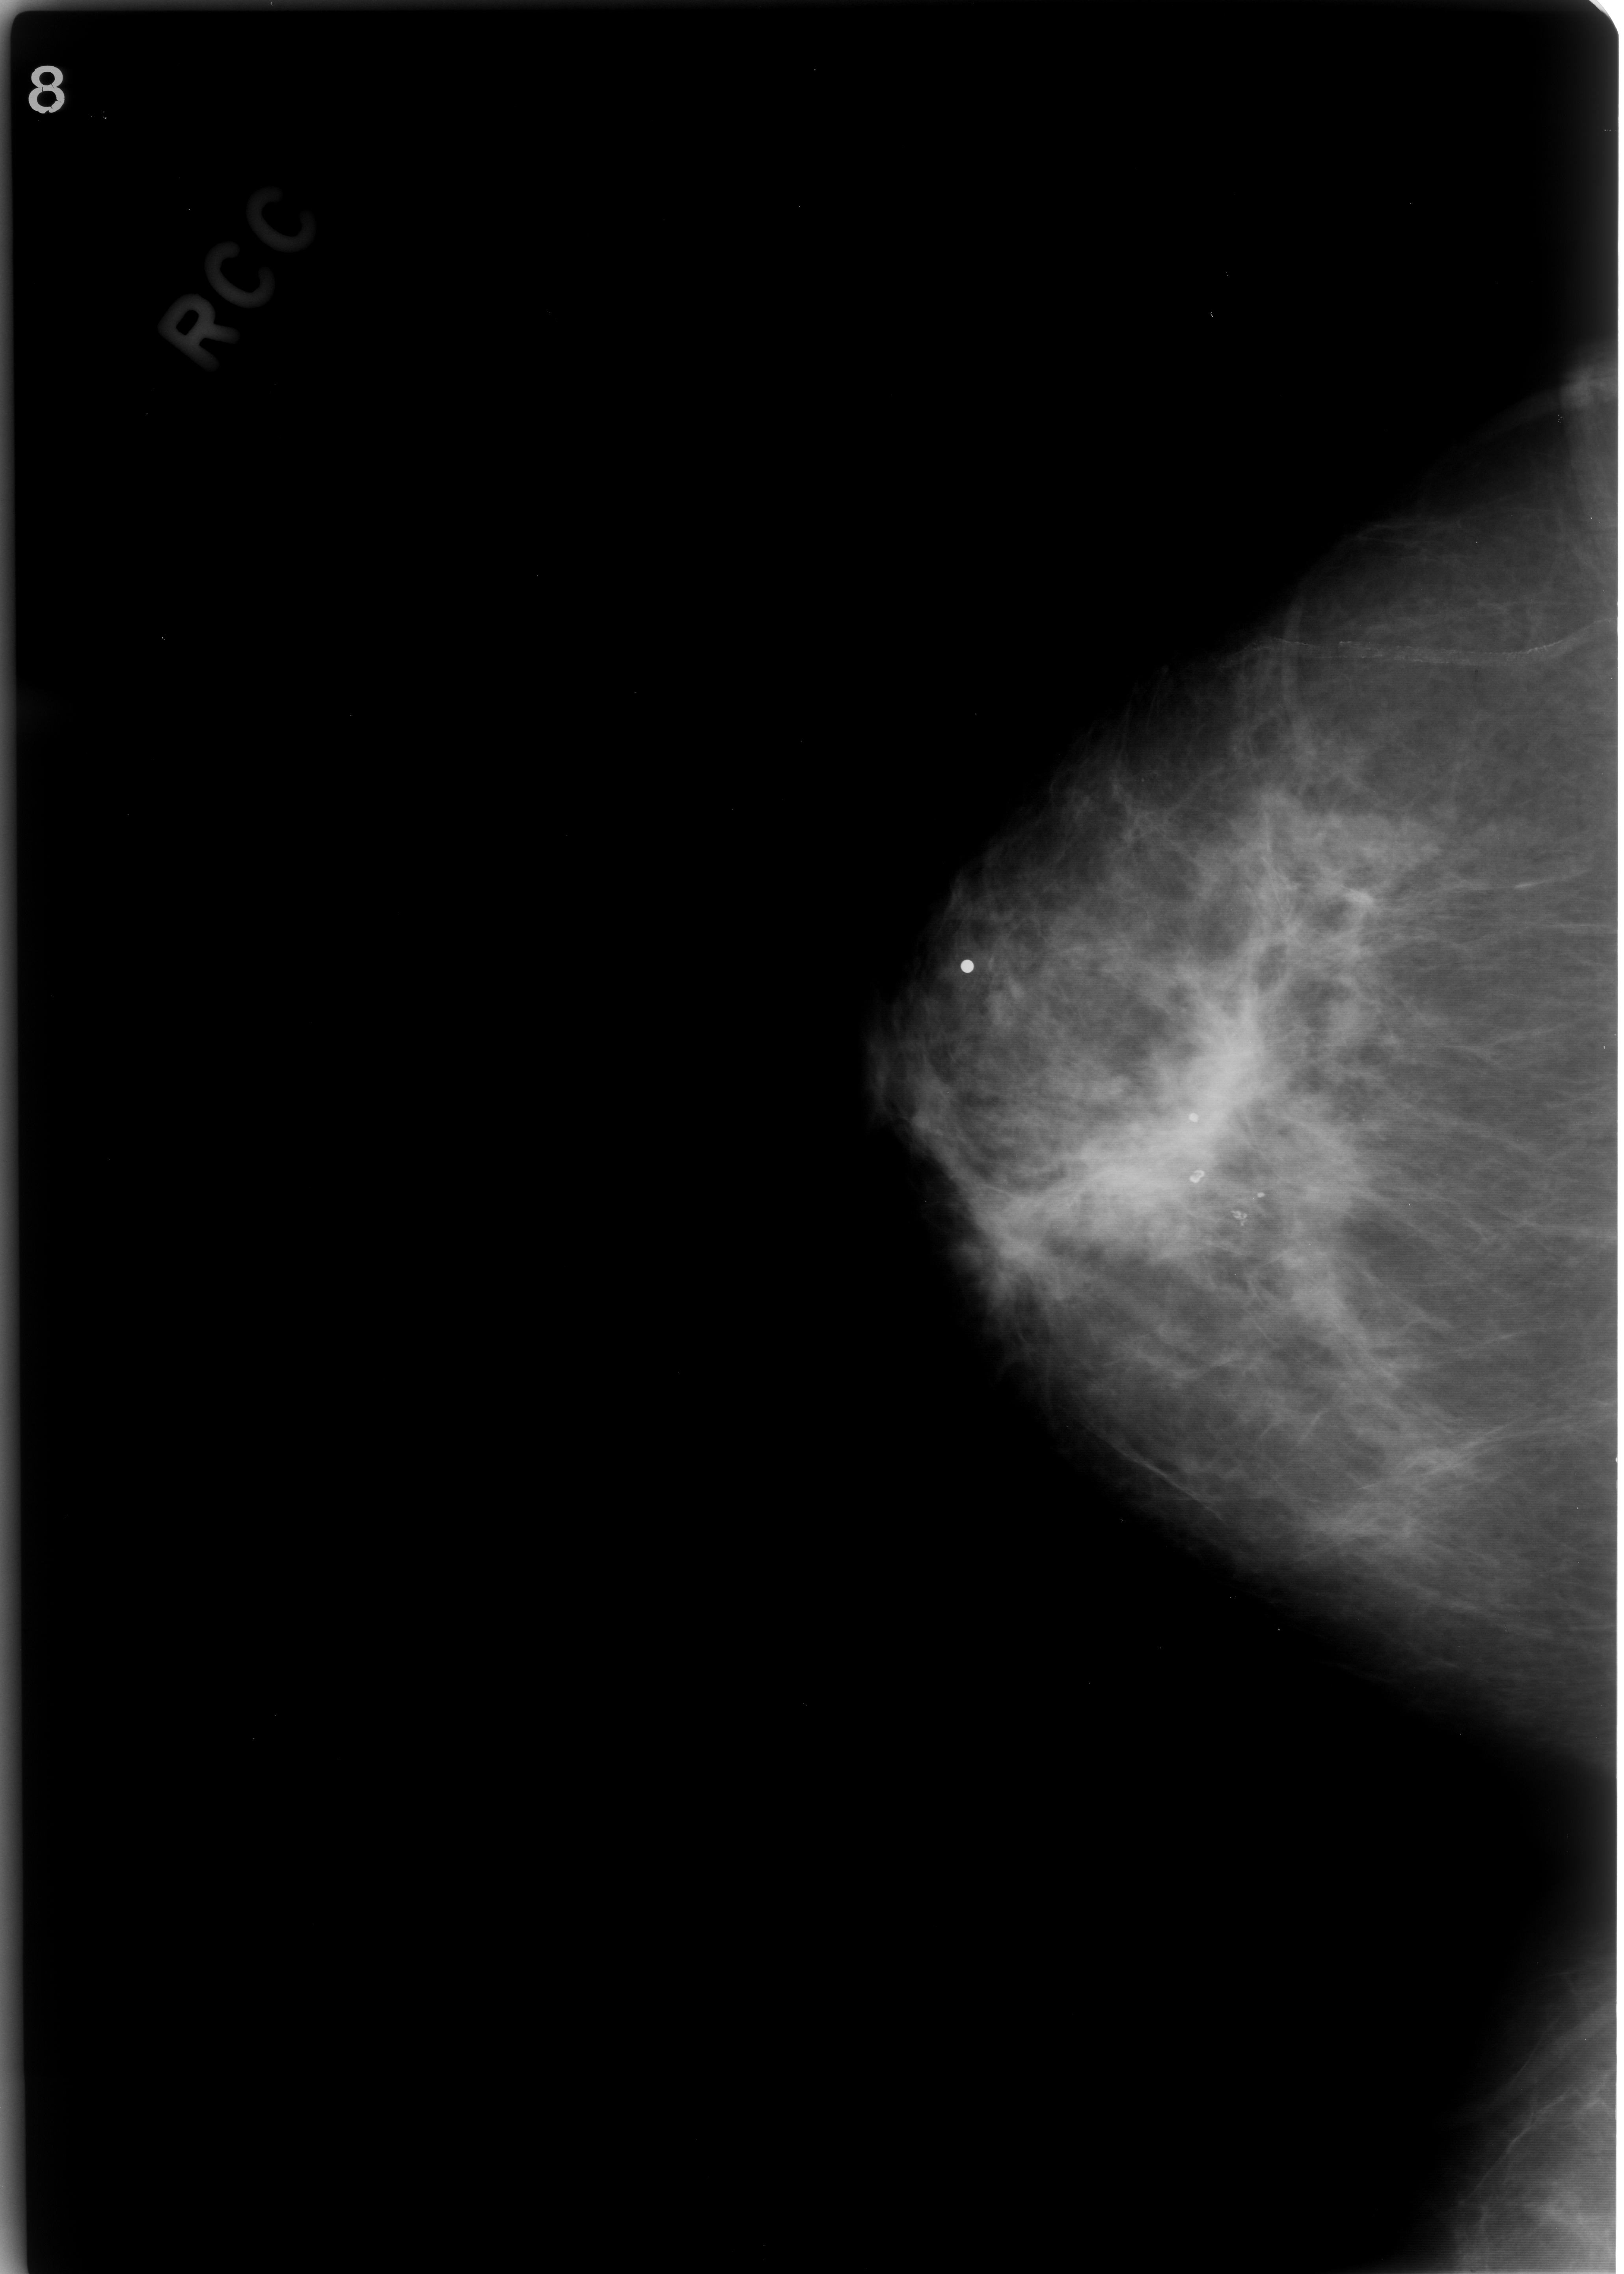
Digitized screen-film mammogram, right breast, craniocaudal (CC) view, BI-RADS breast density category 2 (scale 1–4).
Marked abnormality: mass, shape asymmetric breast tissue, margins ill defined; BI-RADS assessment category 5; subtlety rating 5 on a 1 (subtle) to 5 (obvious) scale; pathology (as recorded): malignant.